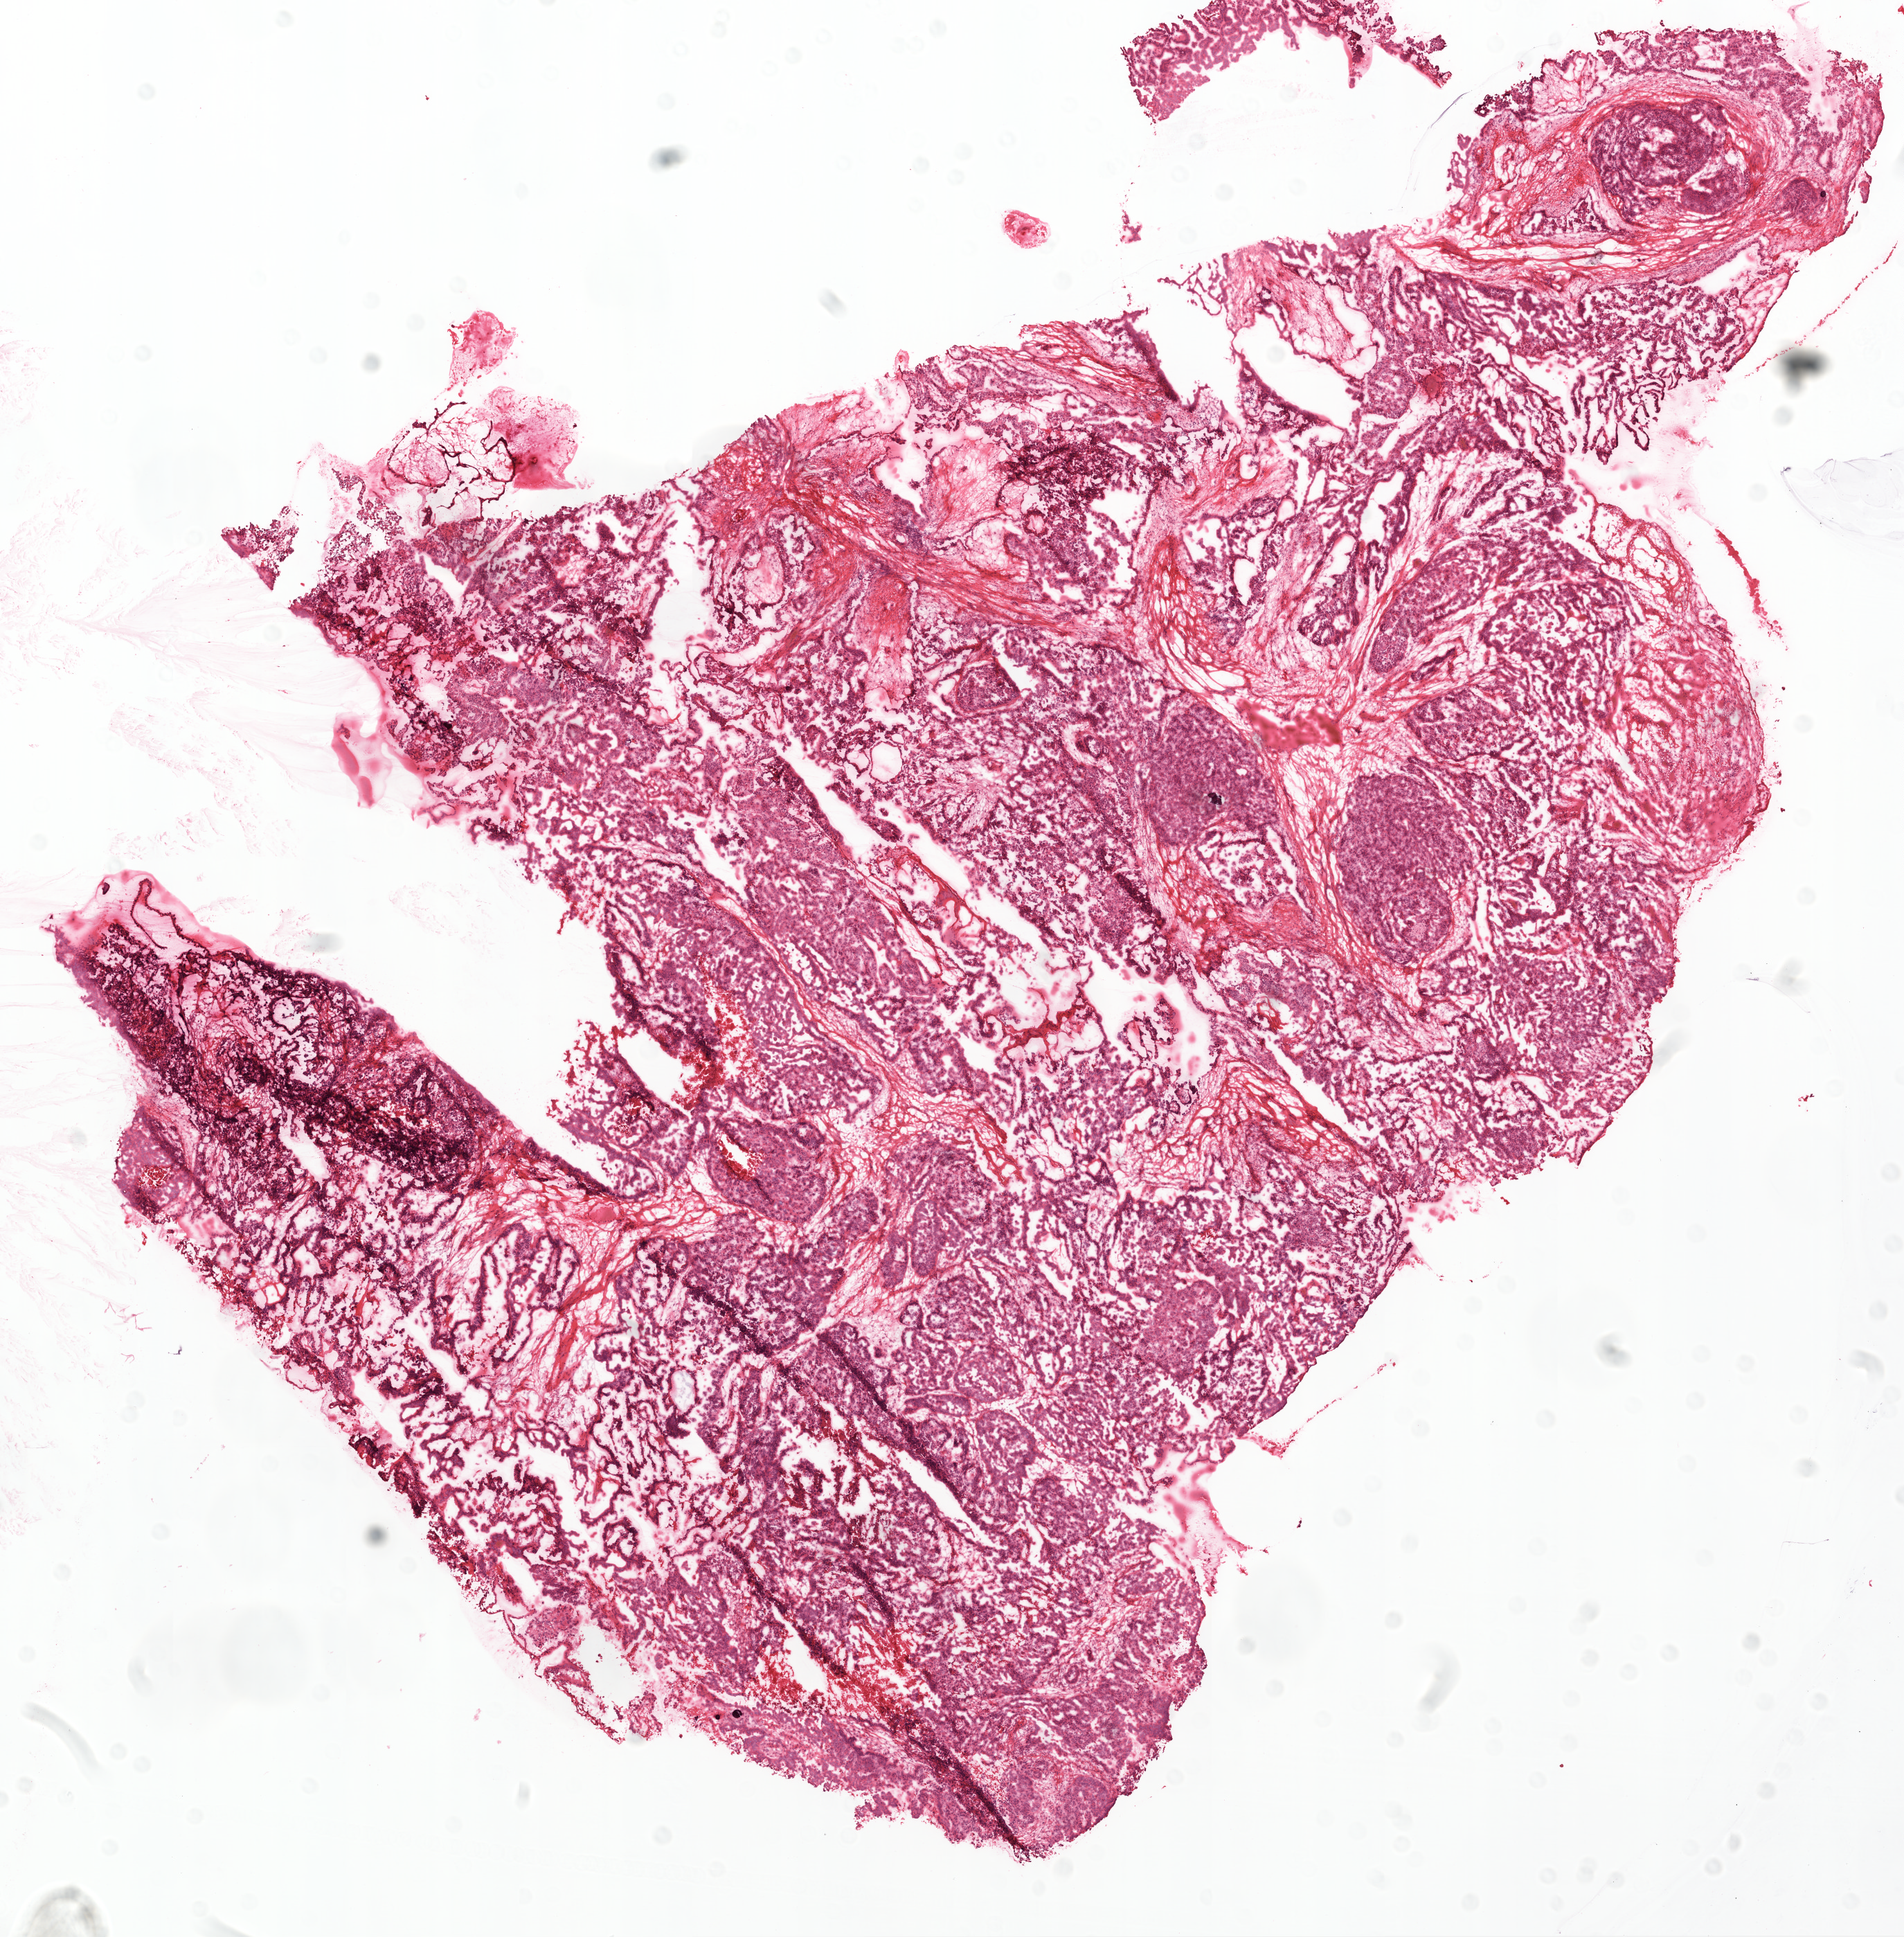
H&E-stained whole-slide image, shown as a low-resolution overview of the whole scanned area (about 11.0 x 11.2 mm, acquisition: 20x scan); frozen section from the top of the tissue portion; ovary, primary tumour sample. Female, age 59 years at initial diagnosis. Histologic grade: G3 (poorly differentiated). Pathologist review of this section (percent, as recorded): tumour cells 90%, tumour nuclei 90%, normal cells 0%, stromal cells 0%, necrosis 10%.
Histologic diagnosis: Serous cystadenocarcinoma, NOS. FIGO stage: IV. Laterality: bilateral.